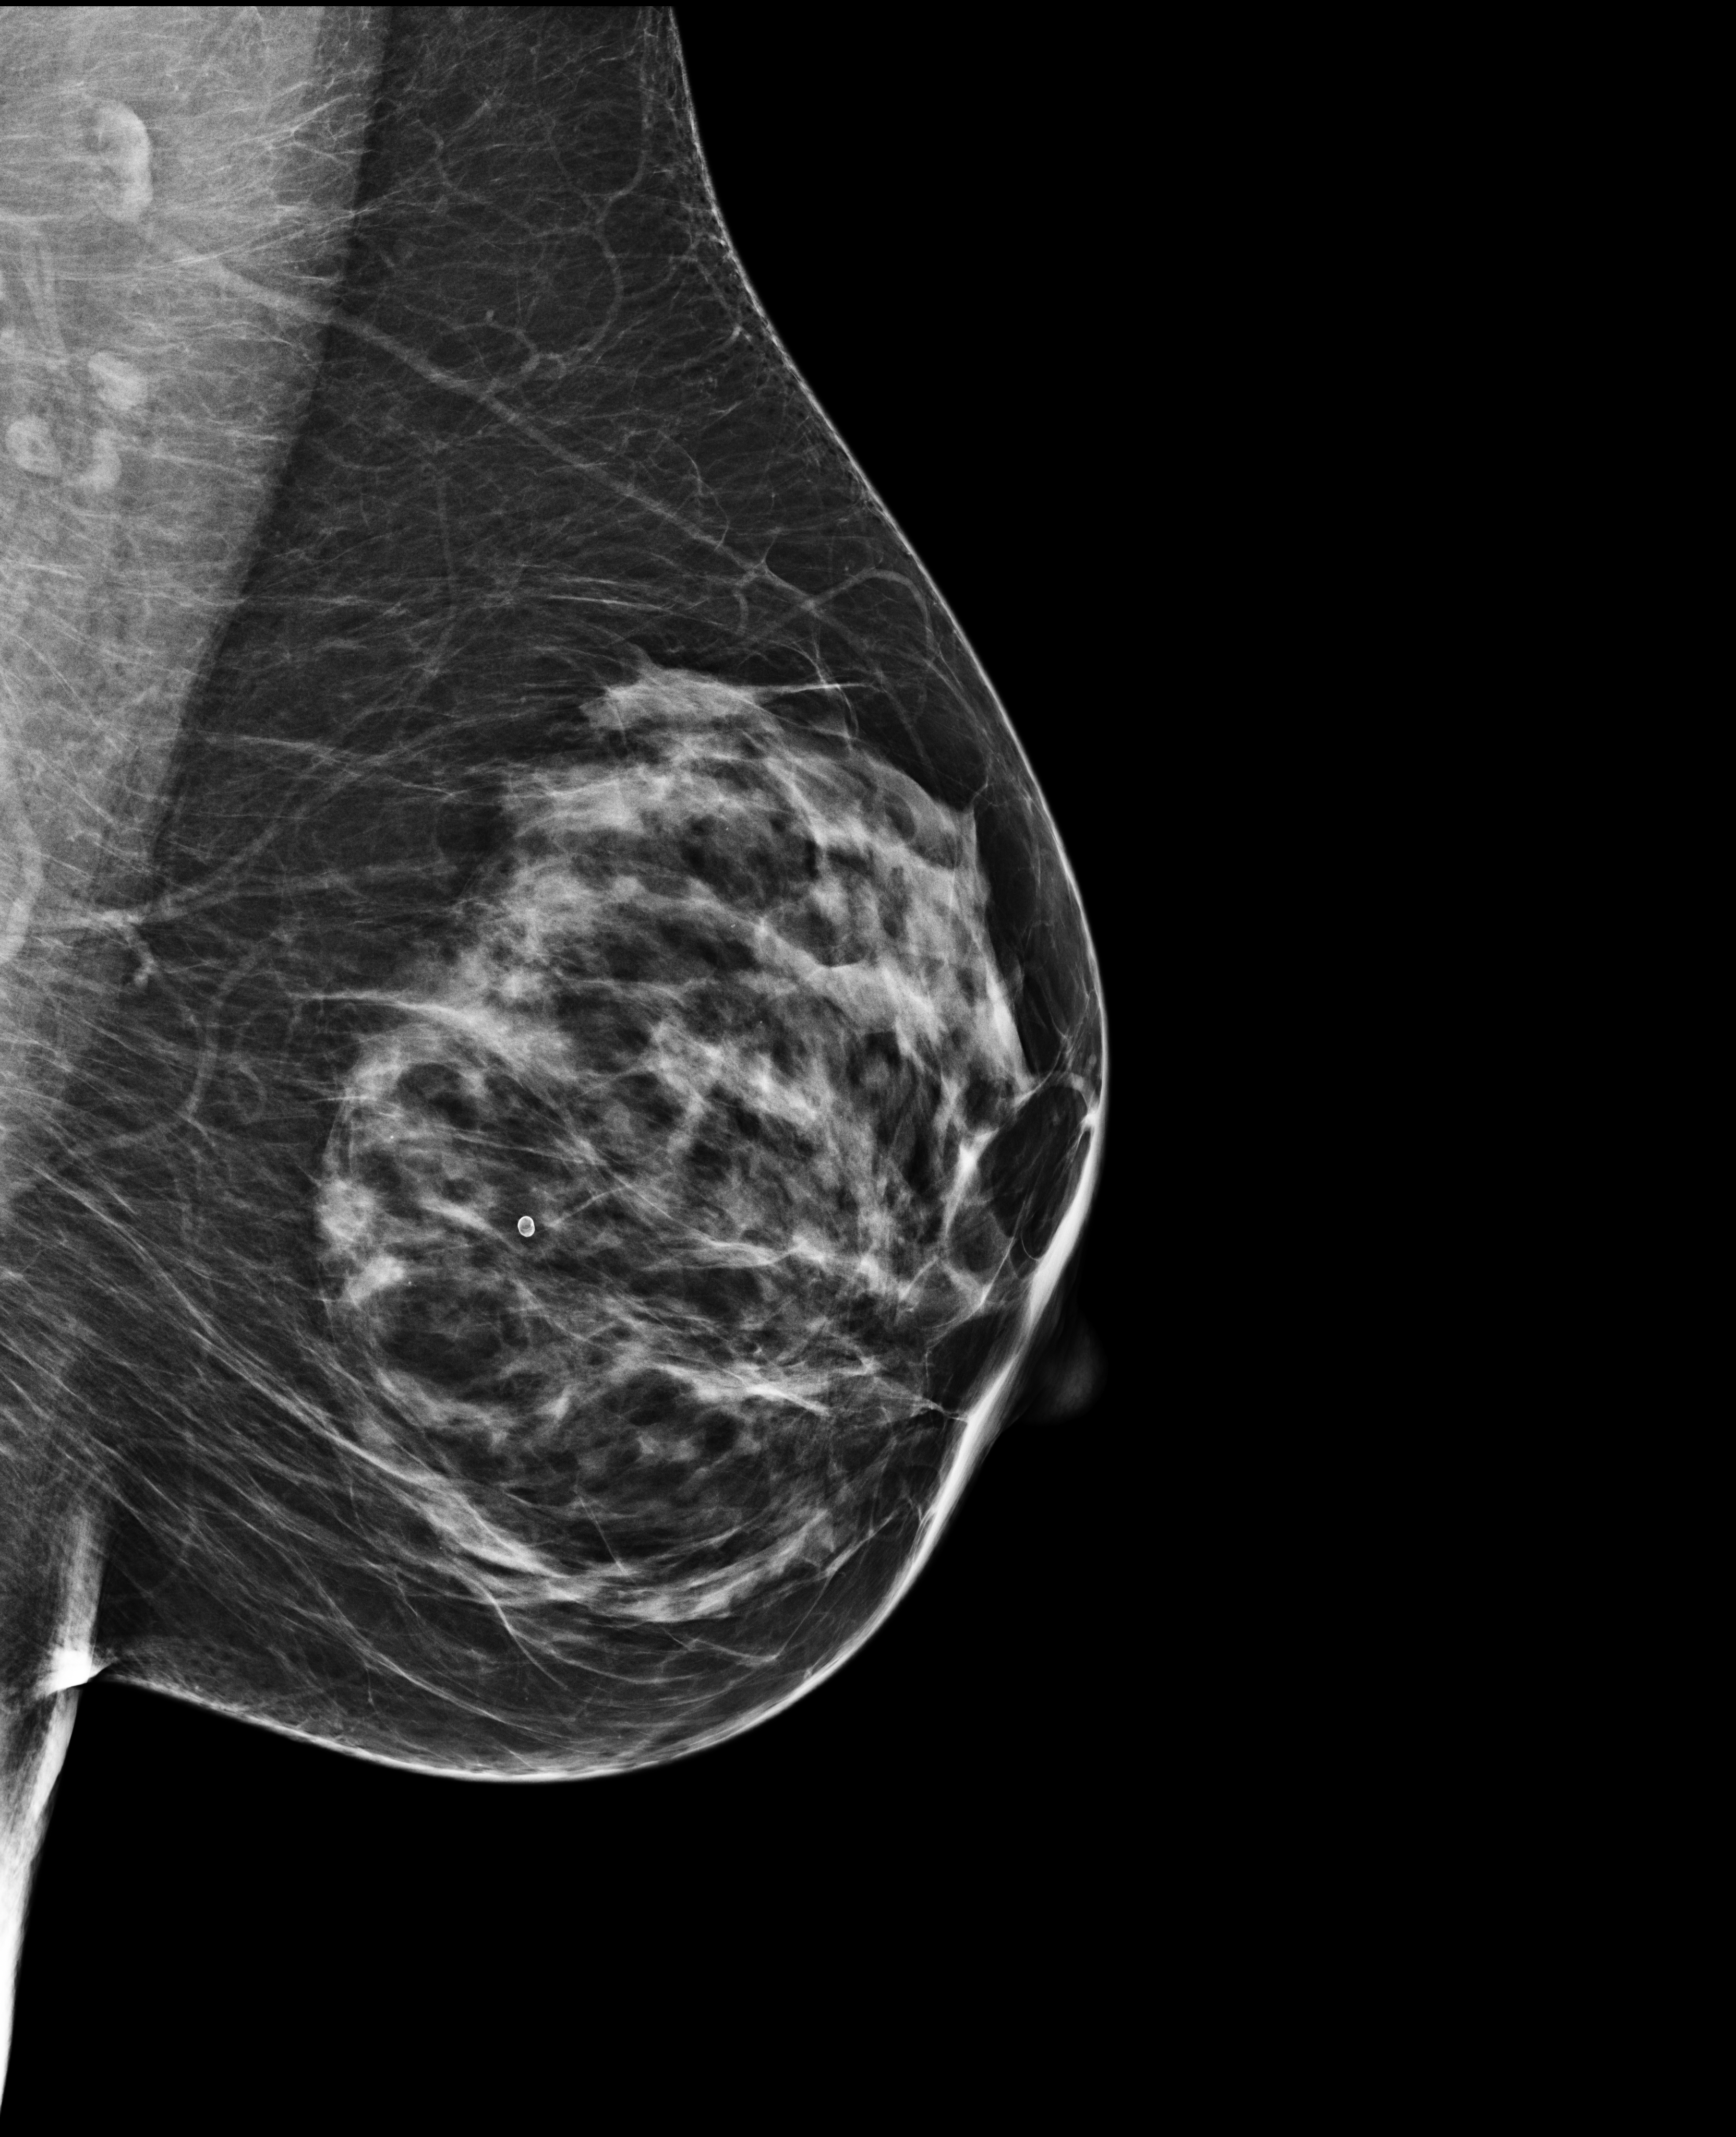
Digital mammogram (FFDM); left breast; mediolateral oblique (MLO) view; annual screening mammography examination. Patient: female, 57 years.
BI-RADS breast density category at the screening exam (both breasts, scale 1–4): 3. Final BI-RADS category for the screening round (tomosynthesis exam, both breasts): category 1. Recall: no recall after this screen.